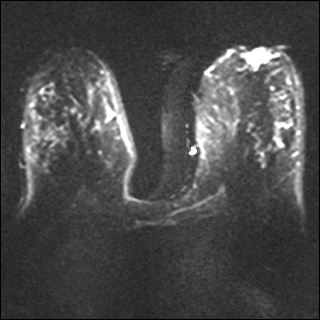
Breast MRI, one axial slice. Slice 19 of 40 in the series (ordered by position). Diffusion-weighted series; image 2 of 4 stored at this slice position (different b-values; order by instance number). 1.5 T. 4 mm slice thickness. 320 × 320 image matrix. Female patient.
Structures marked on this image (expert manual segmentation):
- tumour on diffusion-weighted imaging: bounding box [x1, y1, x2, y2] px = [248, 50, 267, 65]